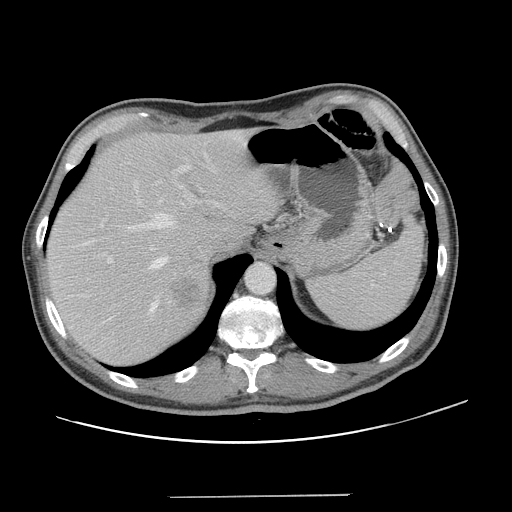
Contrast-enhanced abdominal CT, one axial slice. Slice 100 of 131 in the series (ordered by position). Soft-tissue window (W 400 / L 40 HU). 2.5 mm slice thickness. 512 × 512 image matrix, field of view 403 × 403 mm. Male patient, age 60 years. Case-level facts recorded for this patient, not image findings: diagnosis: colorectal cancer liver metastases, imaged before liver resection; multiple liver metastases: no; largest metastasis: 2.5 cm; disease in both lobes: no.
Outlined on this slice (outlined manually by an expert reader):
- hepatic veins: bounding box <83,170,216,313> (left, top, right, bottom; pixels)
- liver: <46,130,278,365>
- planned liver remnant (the part of the liver to remain after resection): <46,130,278,352>
- portal vein (with intrahepatic branches): <95,151,223,264>
- liver metastasis: <173,278,202,309>